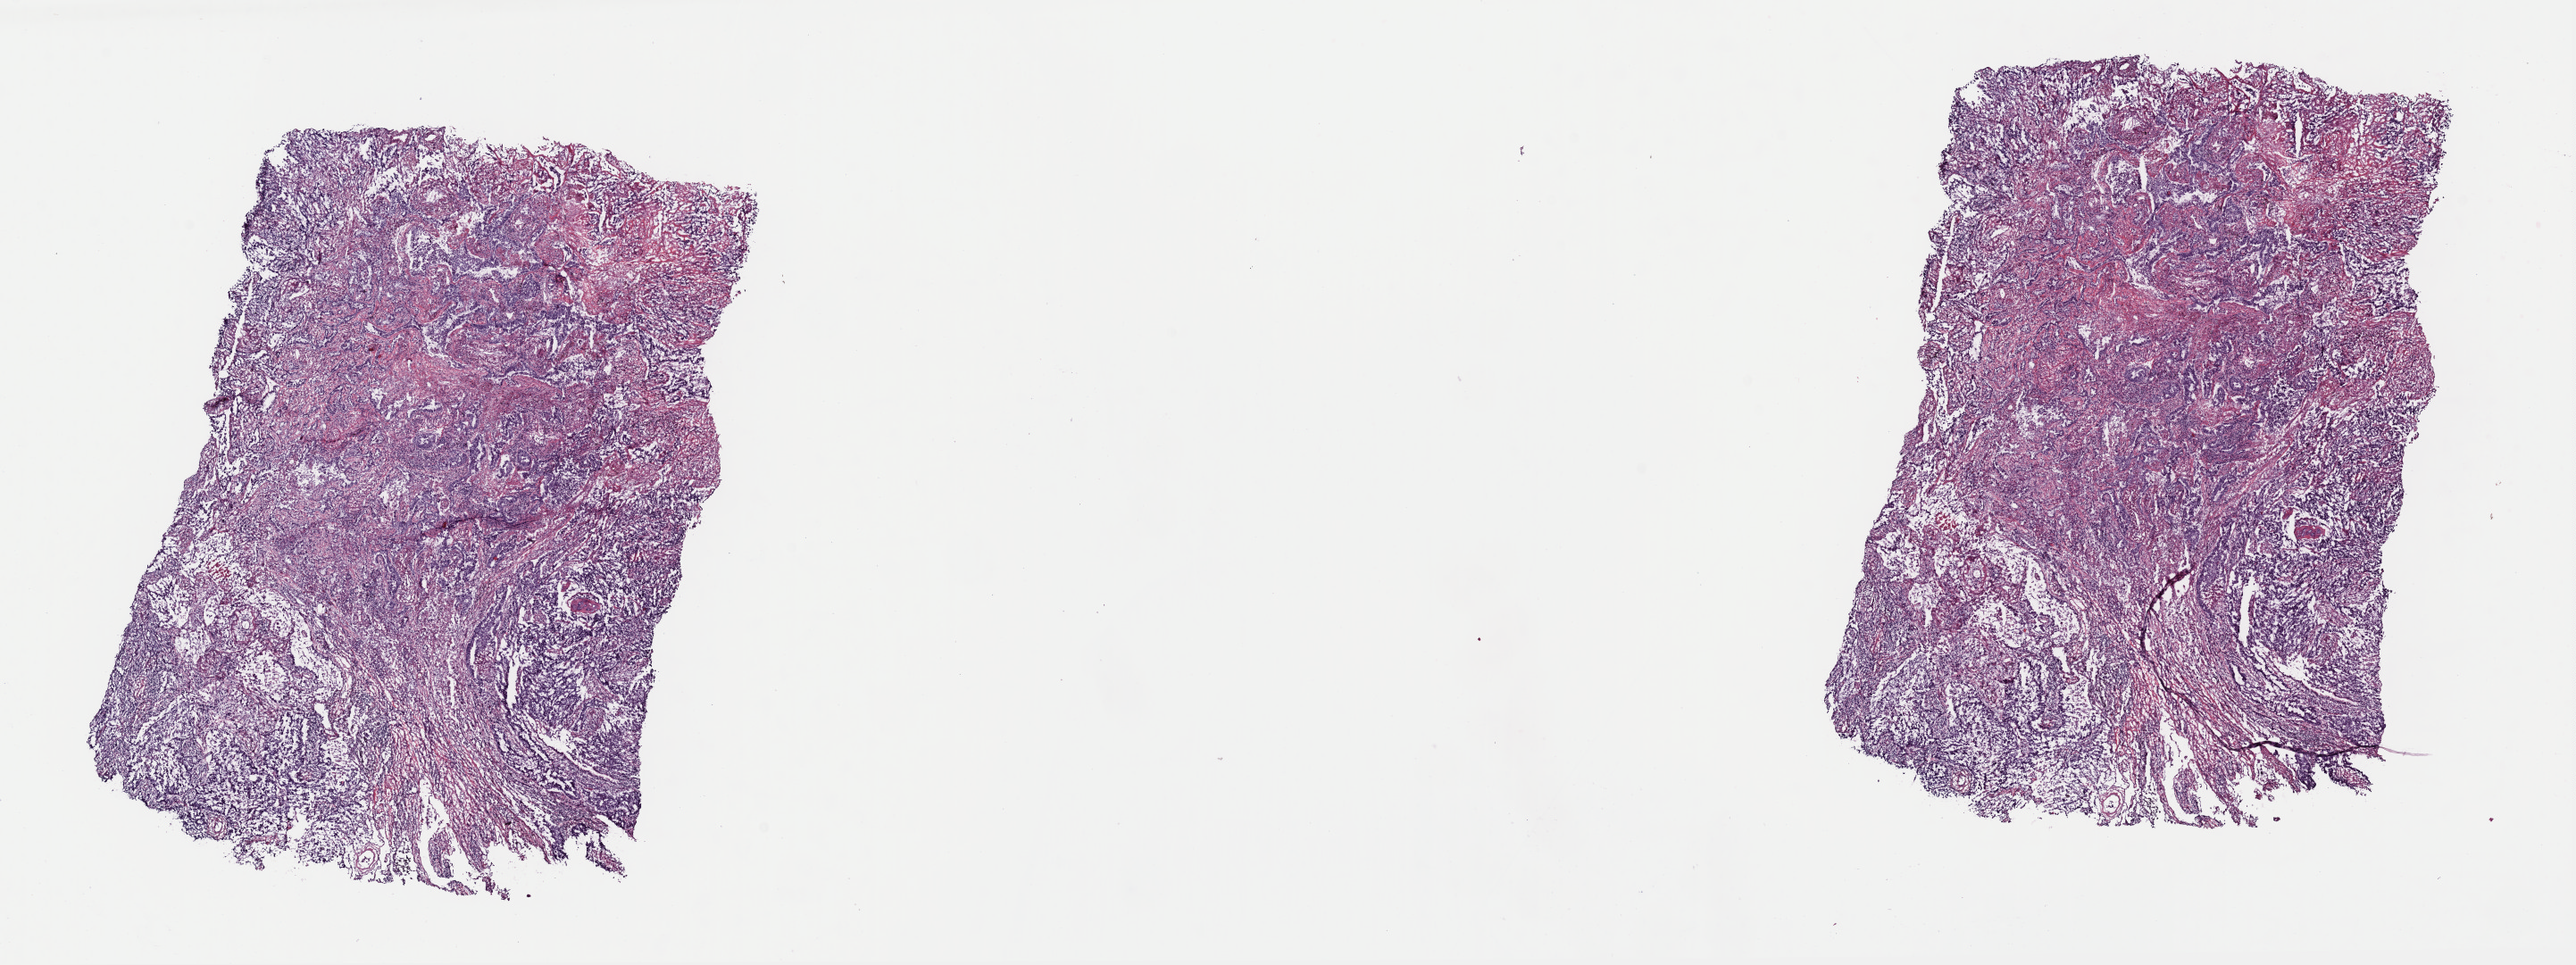
Whole-slide histology image, Hematoxylin and eosin (H&E) stained, a low-resolution overview of the entire scanned area, about 22.8 x 8.5 mm; frozen section from the top of the tissue portion; sample: primary tumour, lung. Patient: male, age at initial diagnosis 67 years. Slide review estimates, as recorded: tumour cells 60%, tumour nuclei 70%, normal cells 0%, stromal cells 40%, necrosis 0%. Inflammatory infiltration, as recorded: lymphocyte infiltration 0%, monocyte infiltration 0%, neutrophil infiltration 0%.
TNM: T2 N0 M0. AJCC pathologic stage: IB (5th edition). Laterality: left. Pathologic diagnosis: Adenocarcinoma, NOS (lower lobe, lung).